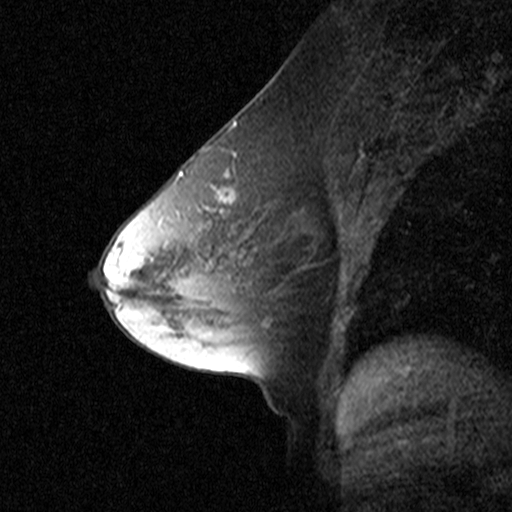
Breast MRI (dynamic contrast-enhanced), one sagittal slice; position 25 of 44 along the scan axis; dynamic contrast-enhanced study with each time point stored as its own series, time point 2 of 3 at this slice position (early post-contrast, ordered by acquisition time); 1.5 T; TE 4.5 ms, TR 11 ms; 3 mm slice thickness; 512 × 512 image matrix, field of view 200 × 200 mm. Female patient, age 53 years. Case-level facts recorded for this patient, not image findings: setting: breast cancer imaged before/during neoadjuvant chemotherapy; receptor status: HR-positive, HER2-negative.
Annotated regions visible in this slice (semi-automatically segmented with operator editing):
- analysis volume of interest (the breast-tissue region the enhancement analysis was run in; not a lesion): bounding box (x1, y1, x2, y2) in pixels: (170, 150, 277, 273)
- tumour enhancement mask (voxels above the 90 % enhancement threshold inside the analysis volume of interest): (178, 172, 238, 212)